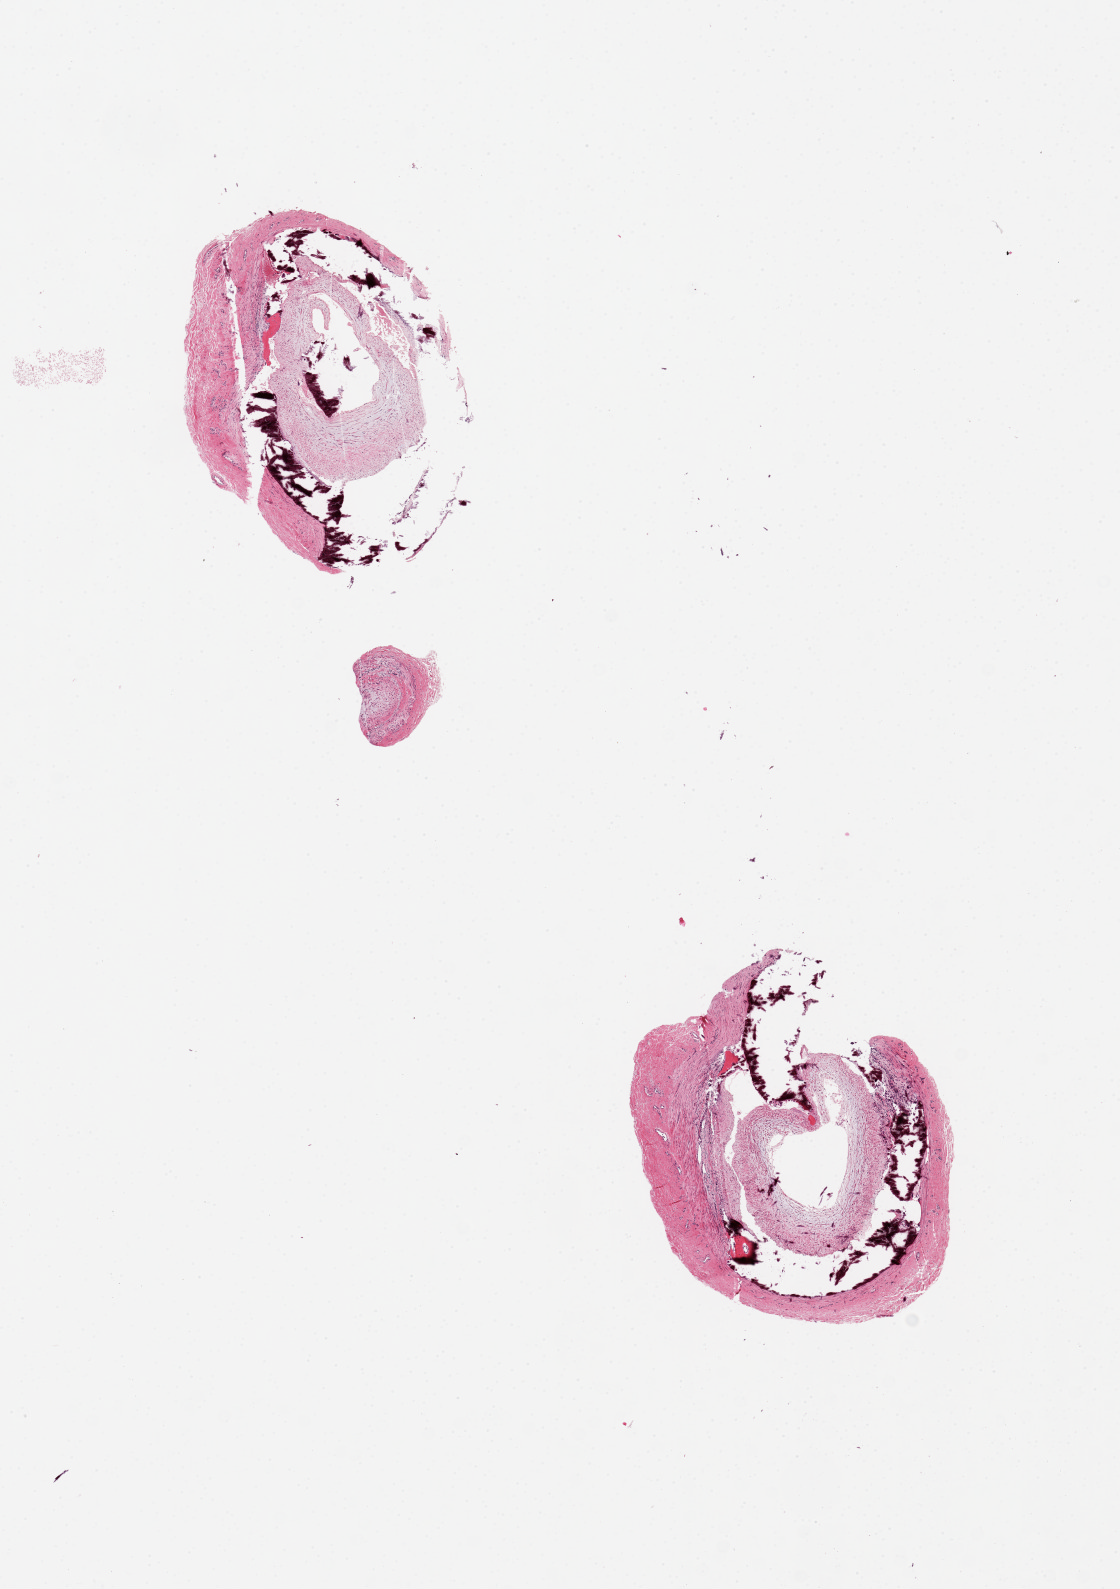
H&E whole-slide image, shown as a low-resolution overview of the whole scanned area (about 8.9 x 12.6 mm, acquisition: 20x scan), PAXgene-fixed paraffin-embedded (PFPE) section, sampled site (target tissue): tibial artery, tissue donor sample. Donor: male.
- pathologist's review note for this sample: 2 pieces, fragmented, due to severe medial calcification with bone formation. Calcific atherosclerosis with narrowing of the lumen